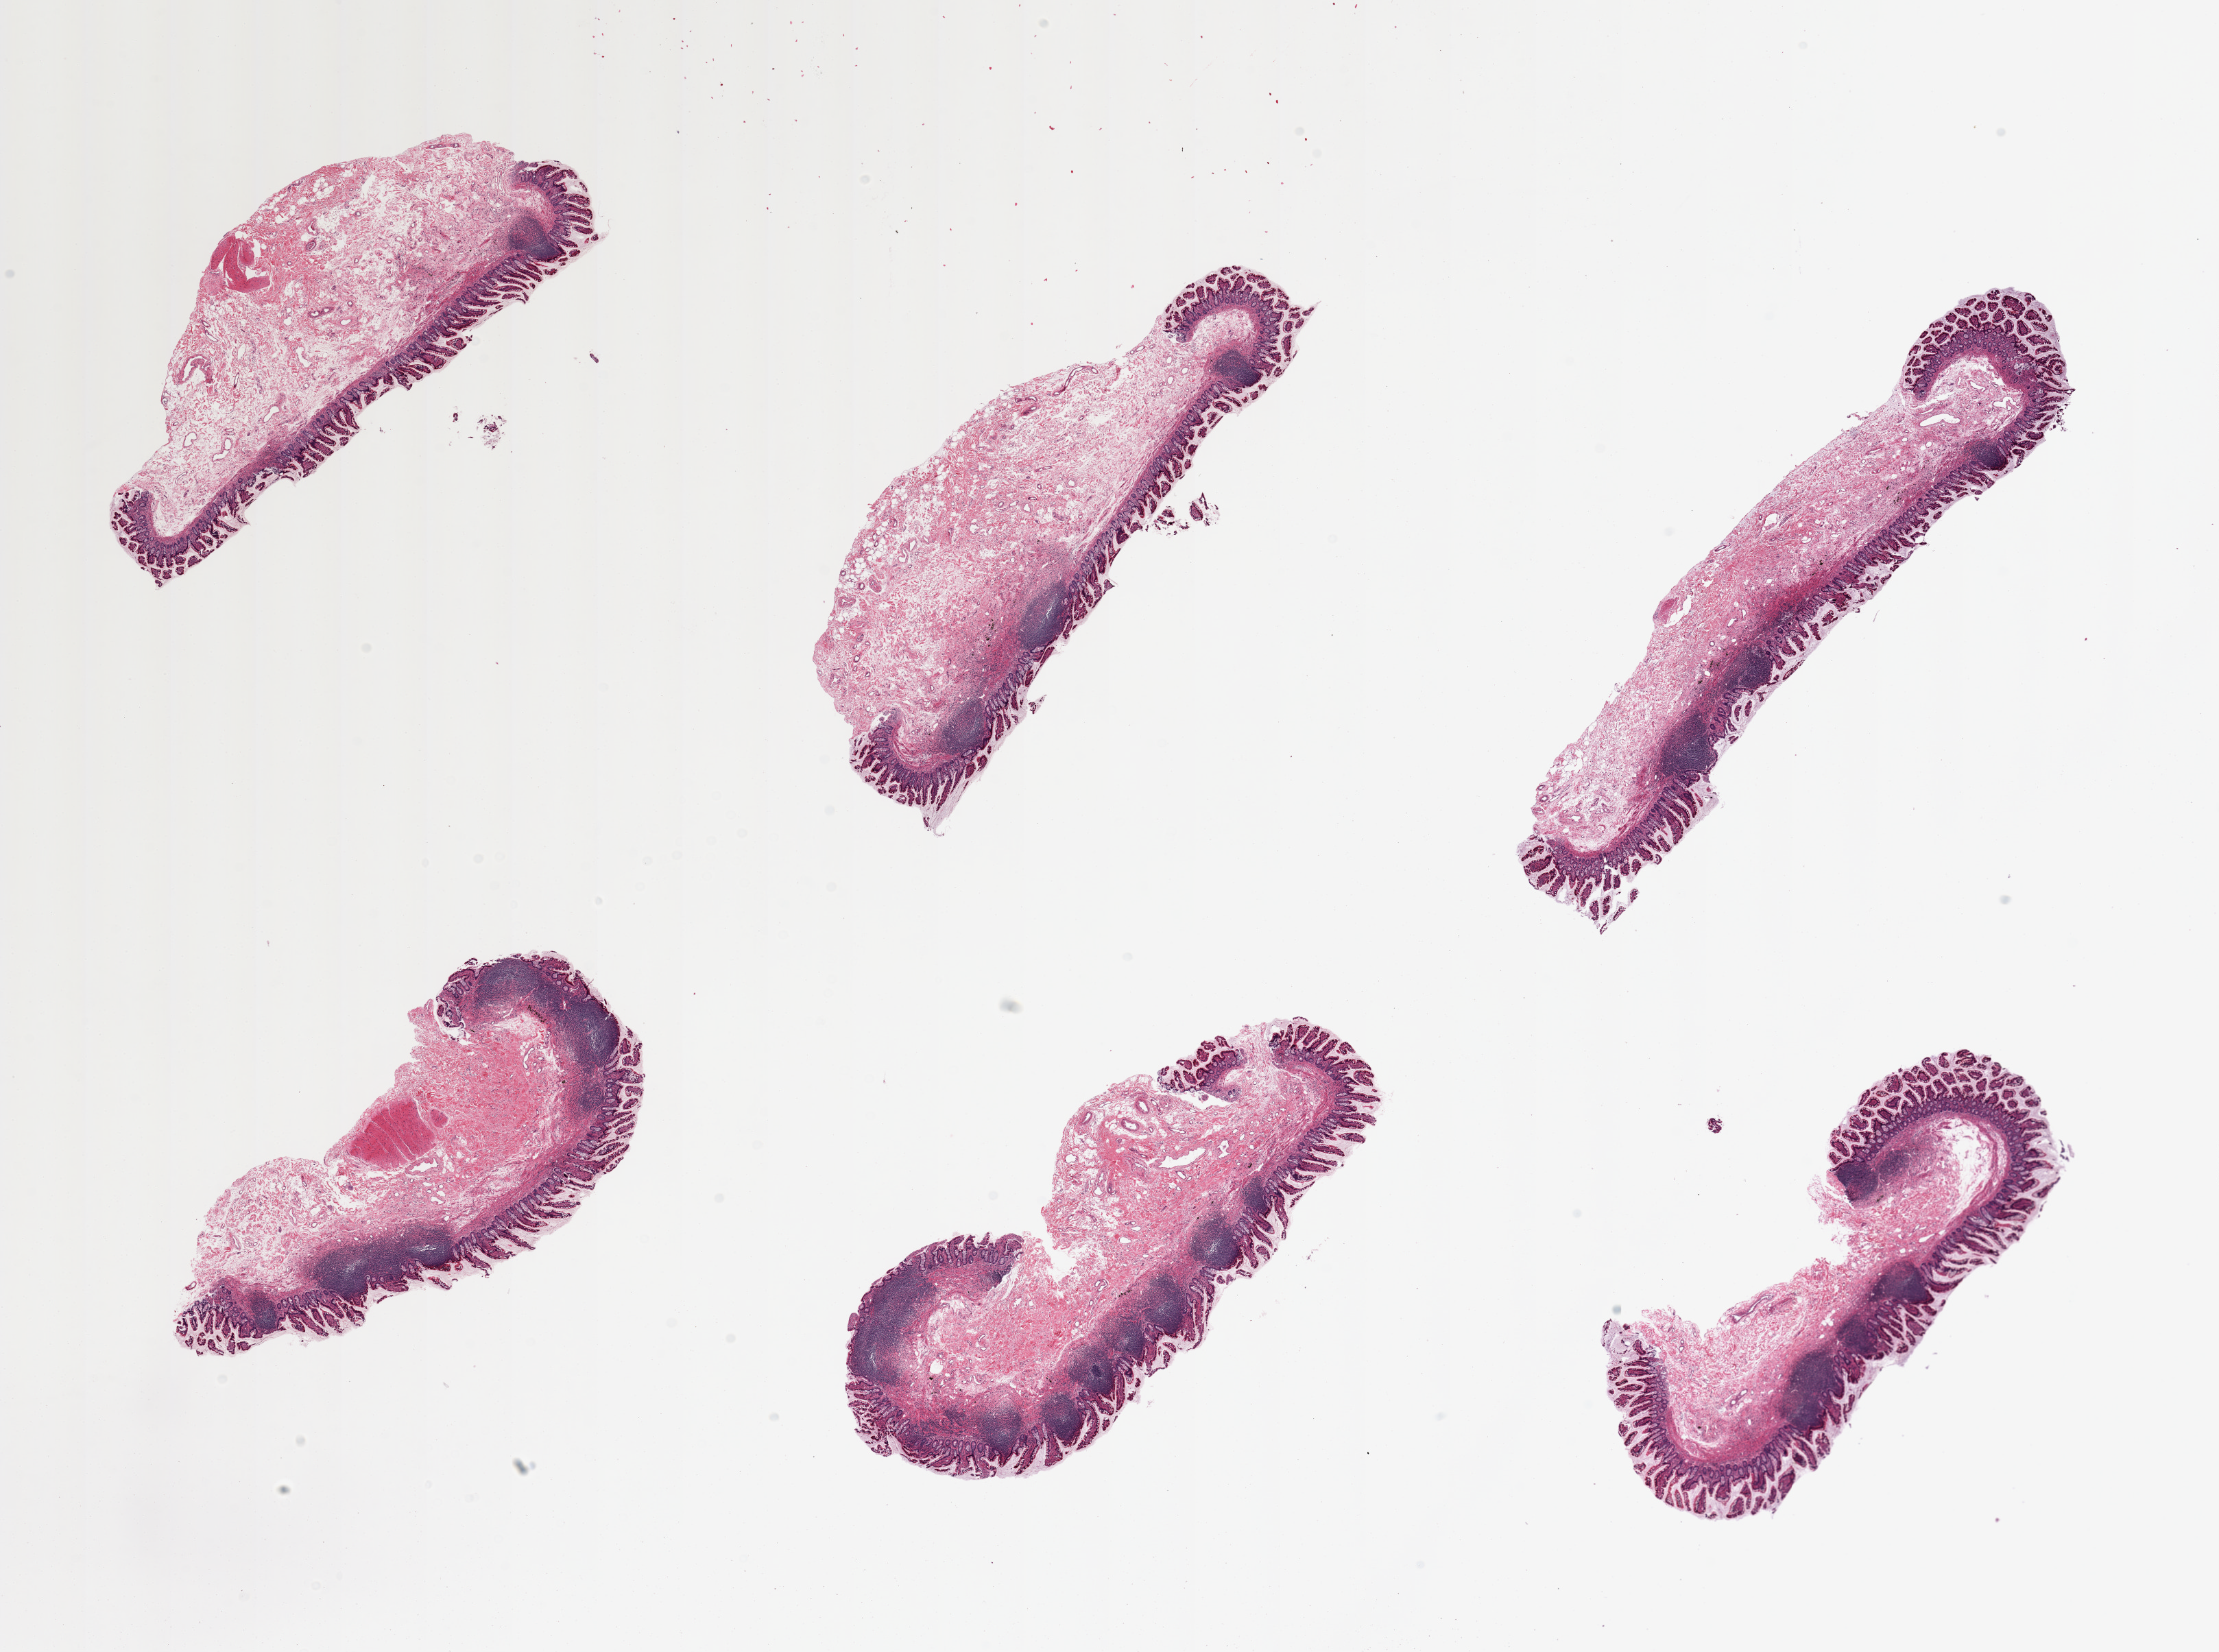
H&E whole-slide image, brightfield — shown as a low-resolution overview of the whole scanned area (about 25.6 x 19.1 mm, slide scanned at 20x); PAXgene-fixed paraffin-embedded (PFPE) section; section of ileum (target tissue); tissue donor sample. Female donor.
Review note (as recorded): 6 pieces, predominantly mucosa and submucosa with small foci of muscularis. Numerous lymphoid aggregates.